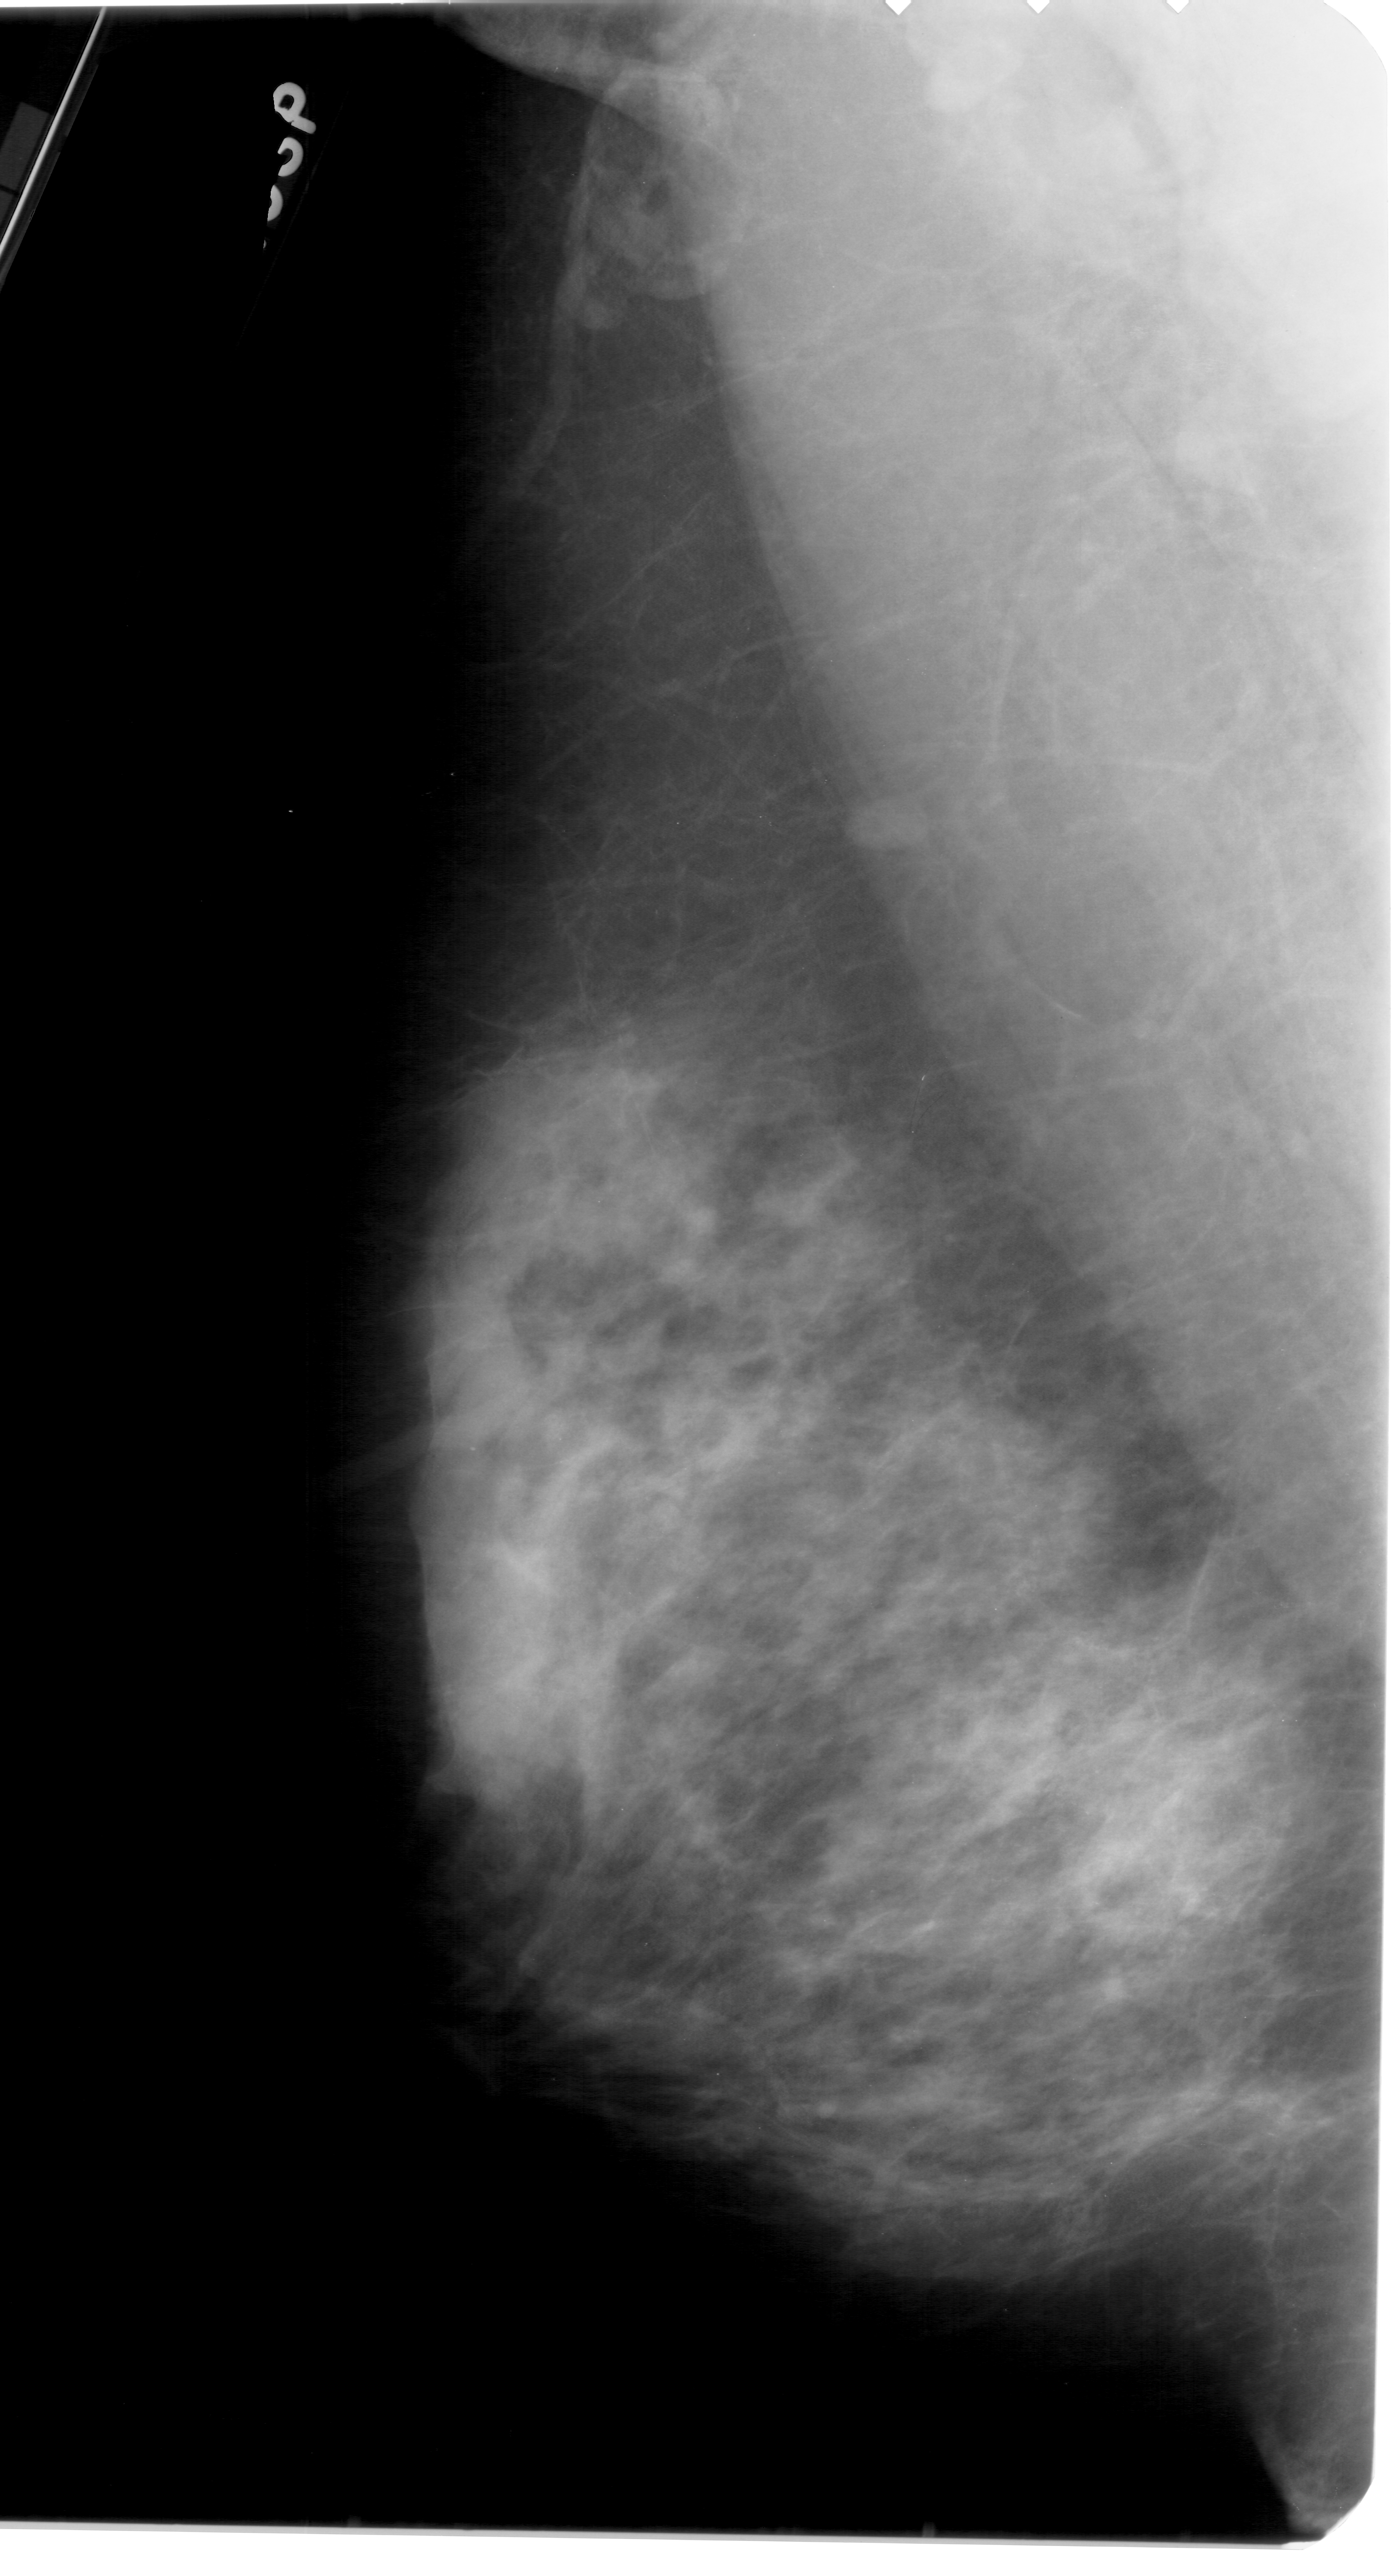
Mammogram (digitized film), left breast, mediolateral oblique (MLO) view, breast composition: heterogeneously dense (BI-RADS density category 3 of 4).
Calcifications, morphology pleomorphic, distribution segmental; BI-RADS assessment category 4; subtlety rating 2 on a 1 (subtle) to 5 (obvious) scale; pathology result (as recorded, not read from the image): benign.